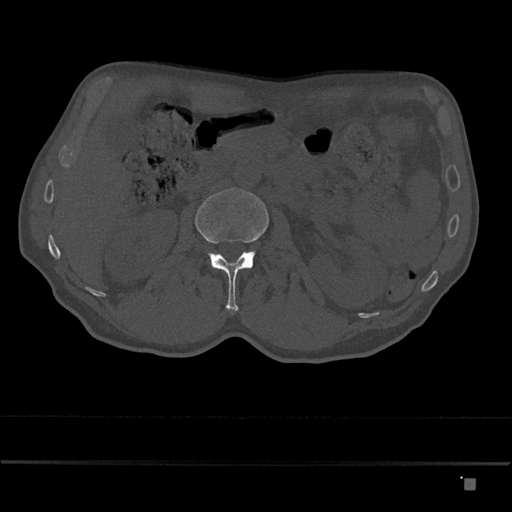
CT including the spine, one axial slice; position 469 of 797 along the scan axis; reconstruction kernel Br40s/3; 120 kVp; bone window (W 1800 / L 400 HU); 512 × 512 image matrix, field of view 390 × 390 mm. Male patient, age 72 years. From the clinical record (not read from this slice): primary cancer: prostate.
Structures marked on this image (semi-automatically segmented with operator editing):
- L2 vertebra: box from (x=195, y=188) to (x=269, y=311) px